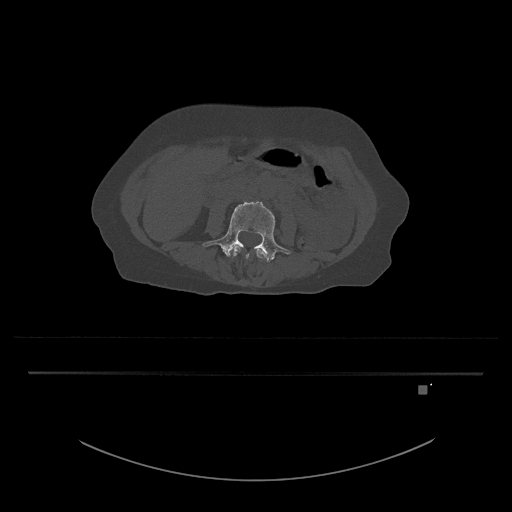
CT including the spine, one axial slice; slice 377 of 797 in the series (ordered by position); reconstruction kernel Br40s/3; 120 kVp; bone window (W 1800 / L 400 HU); 0.5 mm slice thickness; 512 × 512 image matrix, field of view 500 × 500 mm. Patient: female, 57 years. From the clinical record (not read from this slice): primary cancer: cervical.
Structures marked on this image (semi-automatic segmentation, software-assisted and operator-edited):
- L3 vertebra: bounding box <232,246,267,259> (left, top, right, bottom; pixels)
- L4 vertebra: <202,201,292,262>